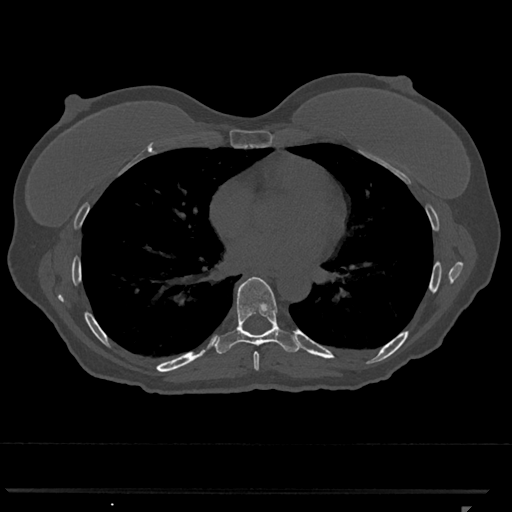
CT including the spine, one axial slice. Position 671 of 793 along the scan axis. Reconstruction kernel Br40s/3. Bone window (W 1800 / L 400 HU). 512 × 512 image matrix, field of view 380 × 380 mm. Patient: female, 62 years. Case-level facts recorded for this patient, not image findings: primary cancer: renal.
Annotated regions visible in this slice (semi-automatically segmented with operator editing):
- T7 vertebra: box from (x=253, y=352) to (x=259, y=371) px
- T8 vertebra: (x=214, y=277)–(x=299, y=354)